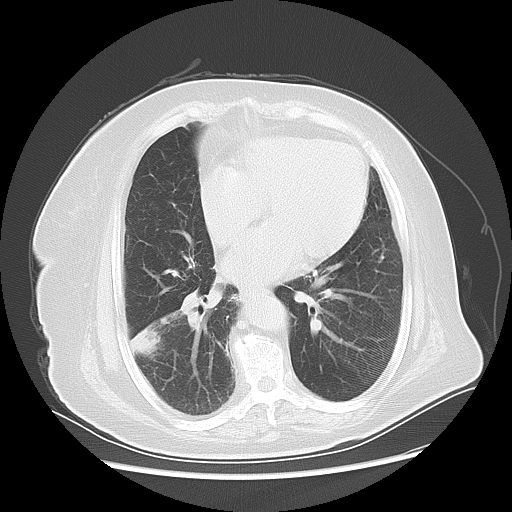
Chest CT, one axial slice; position 24 of 56 along the scan axis; 120 kVp; lung window (W 1500 / L -600 HU); 5 mm slice thickness; 512 × 512 image matrix. Patient: female, 73 years. From the clinical record (not read from this slice): clinical TNM (as recorded): T3 N0 M0.
Structures marked on this image (rectangle marked by the reading radiologist):
- lung tumour (recorded histology: adenocarcinoma): bounding box <125,323,165,359> (left, top, right, bottom; pixels)